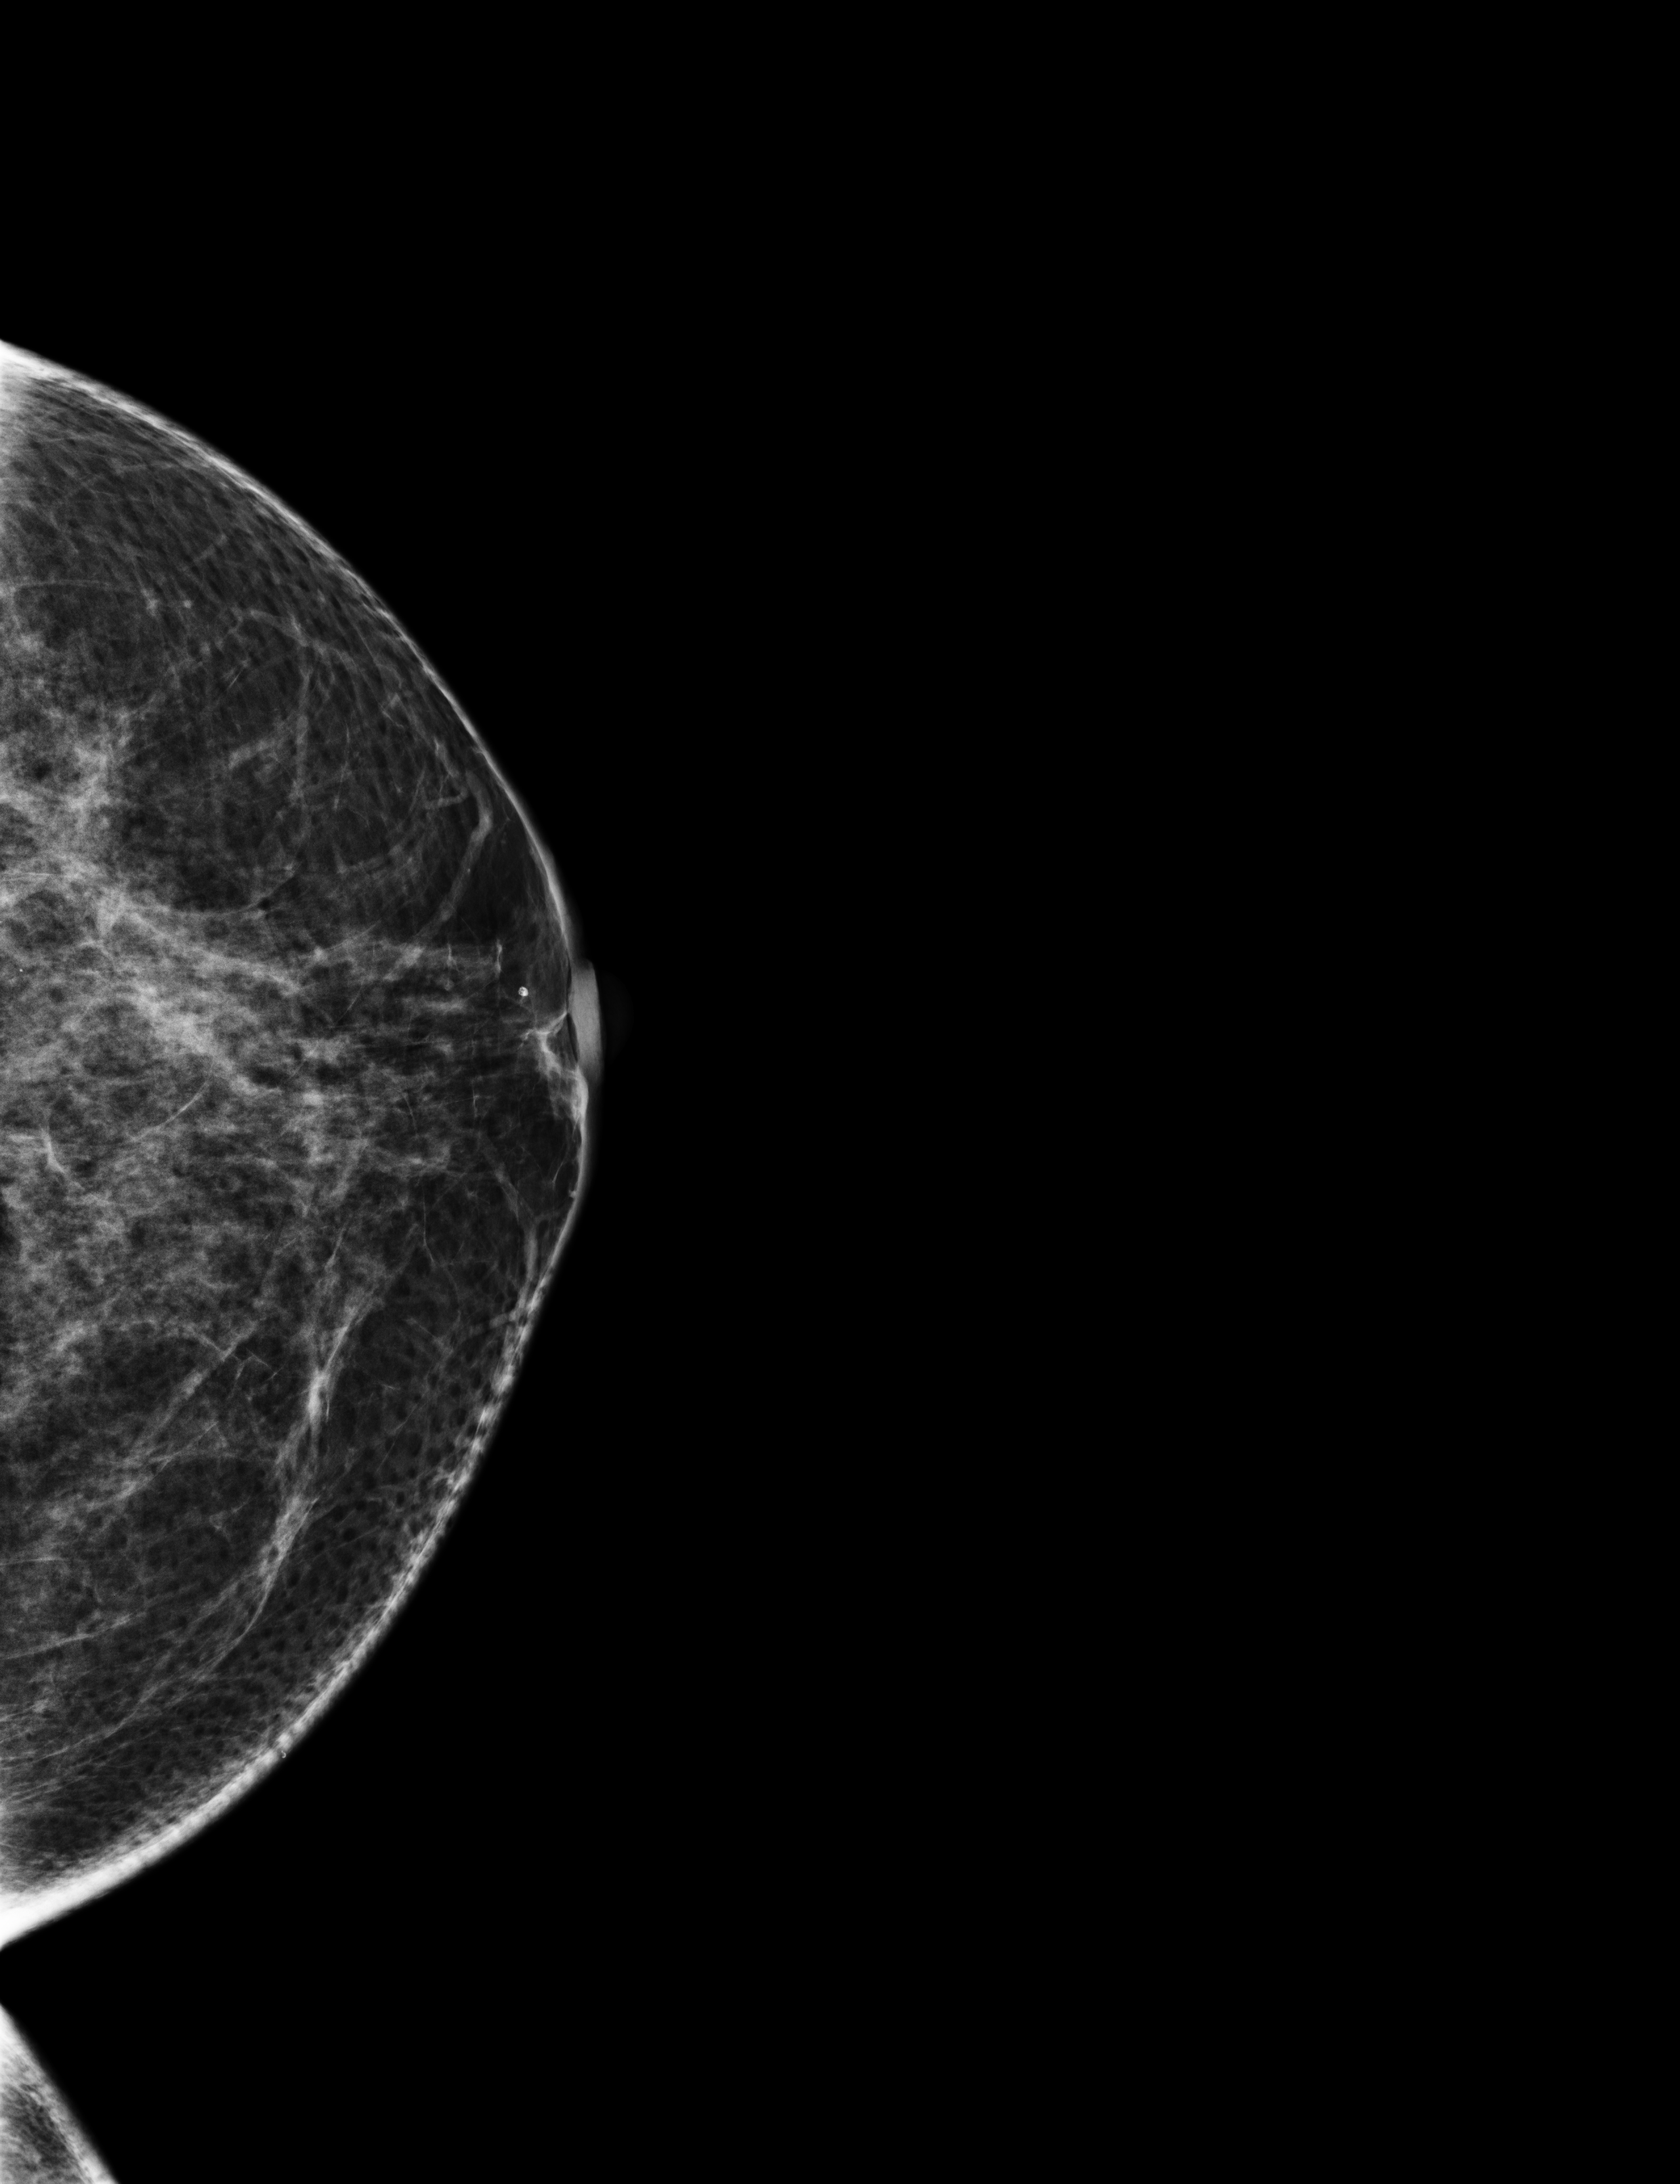
Annual screening mammography examination.
Image type: full-field digital mammogram. Breast: left. Projection: craniocaudal (CC) view.